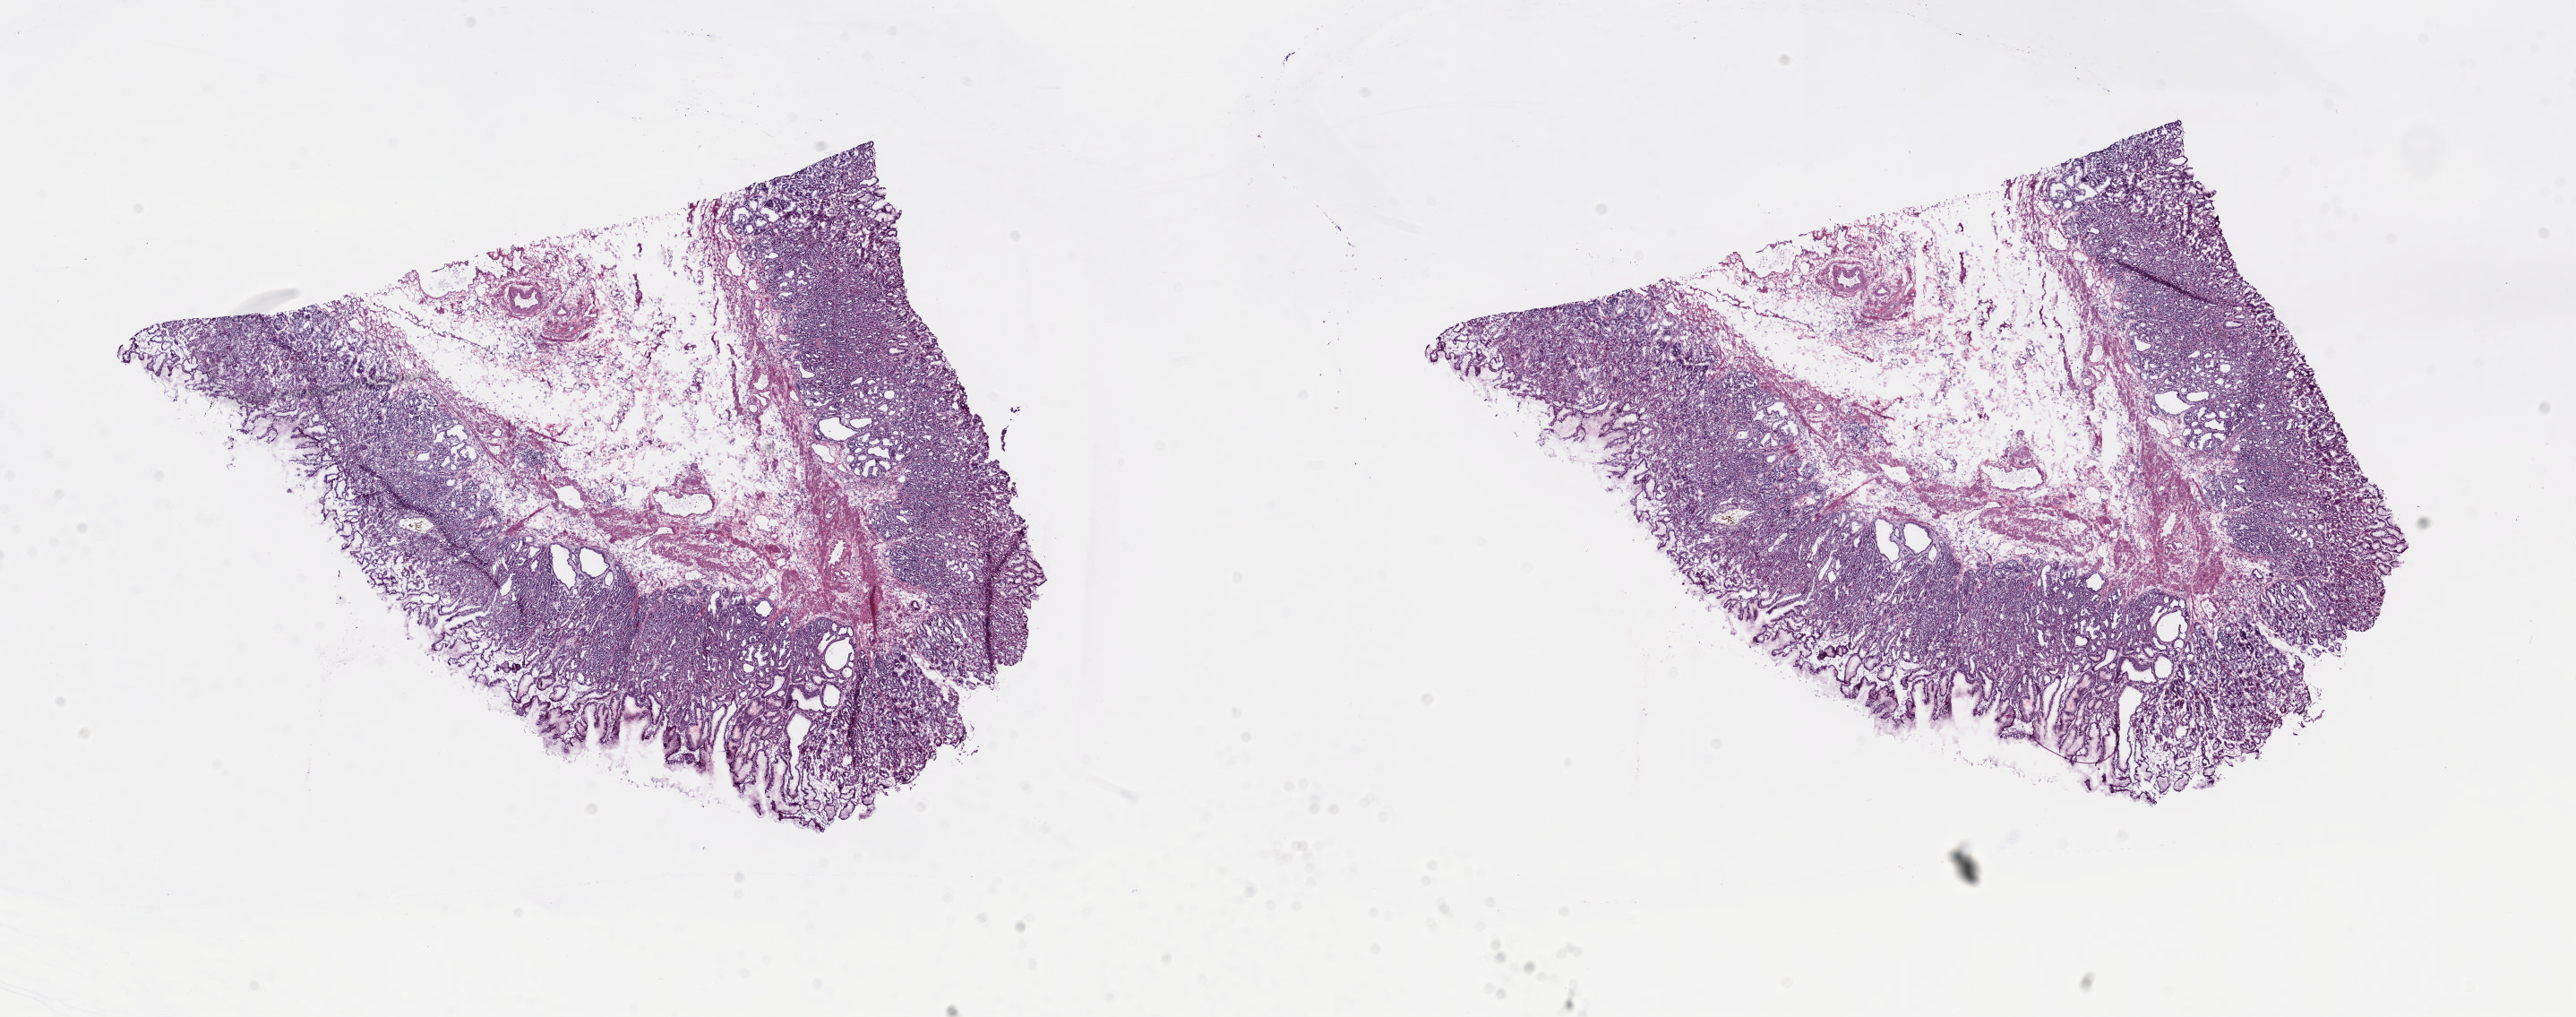
Digitized H&E tissue section (whole slide), a low-resolution overview of the entire scanned area, about 22.8 x 9.0 mm (acquisition: 20x scan). Frozen section from the top of the tissue portion. Sample: solid tissue normal (non-tumour tissue), esophagus. Patient: male, age at initial diagnosis 81 years. Composition of this section per pathologist review: tumour cells 0%, tumour nuclei 0%, normal cells 100%, stromal cells 0%, necrosis 0%. Infiltration values recorded for this section: lymphocyte infiltration 0%, monocyte infiltration 0%, neutrophil infiltration 0%.
- this section: solid tissue normal sample (biorepository sample class)
- patient diagnosis: Adenocarcinoma, NOS (lower third of esophagus)